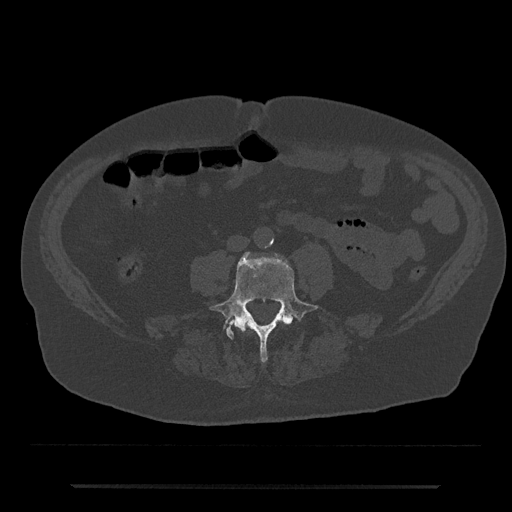
CT including the spine, one axial slice. Slice 355 of 797 in the series (ordered by position). 120 kVp. Bone window (W 1800 / L 400 HU). 0.5 mm slice thickness. 512 × 512 image matrix. Male patient, age 80 years. From the clinical record (not read from this slice): primary cancer: prostate.
Outlined on this slice (semi-automatic segmentation, software-assisted and operator-edited):
- L3 vertebra: bounding box (x1, y1, x2, y2) in pixels: (243, 320, 286, 329)
- L4 vertebra: (209, 252, 319, 363)